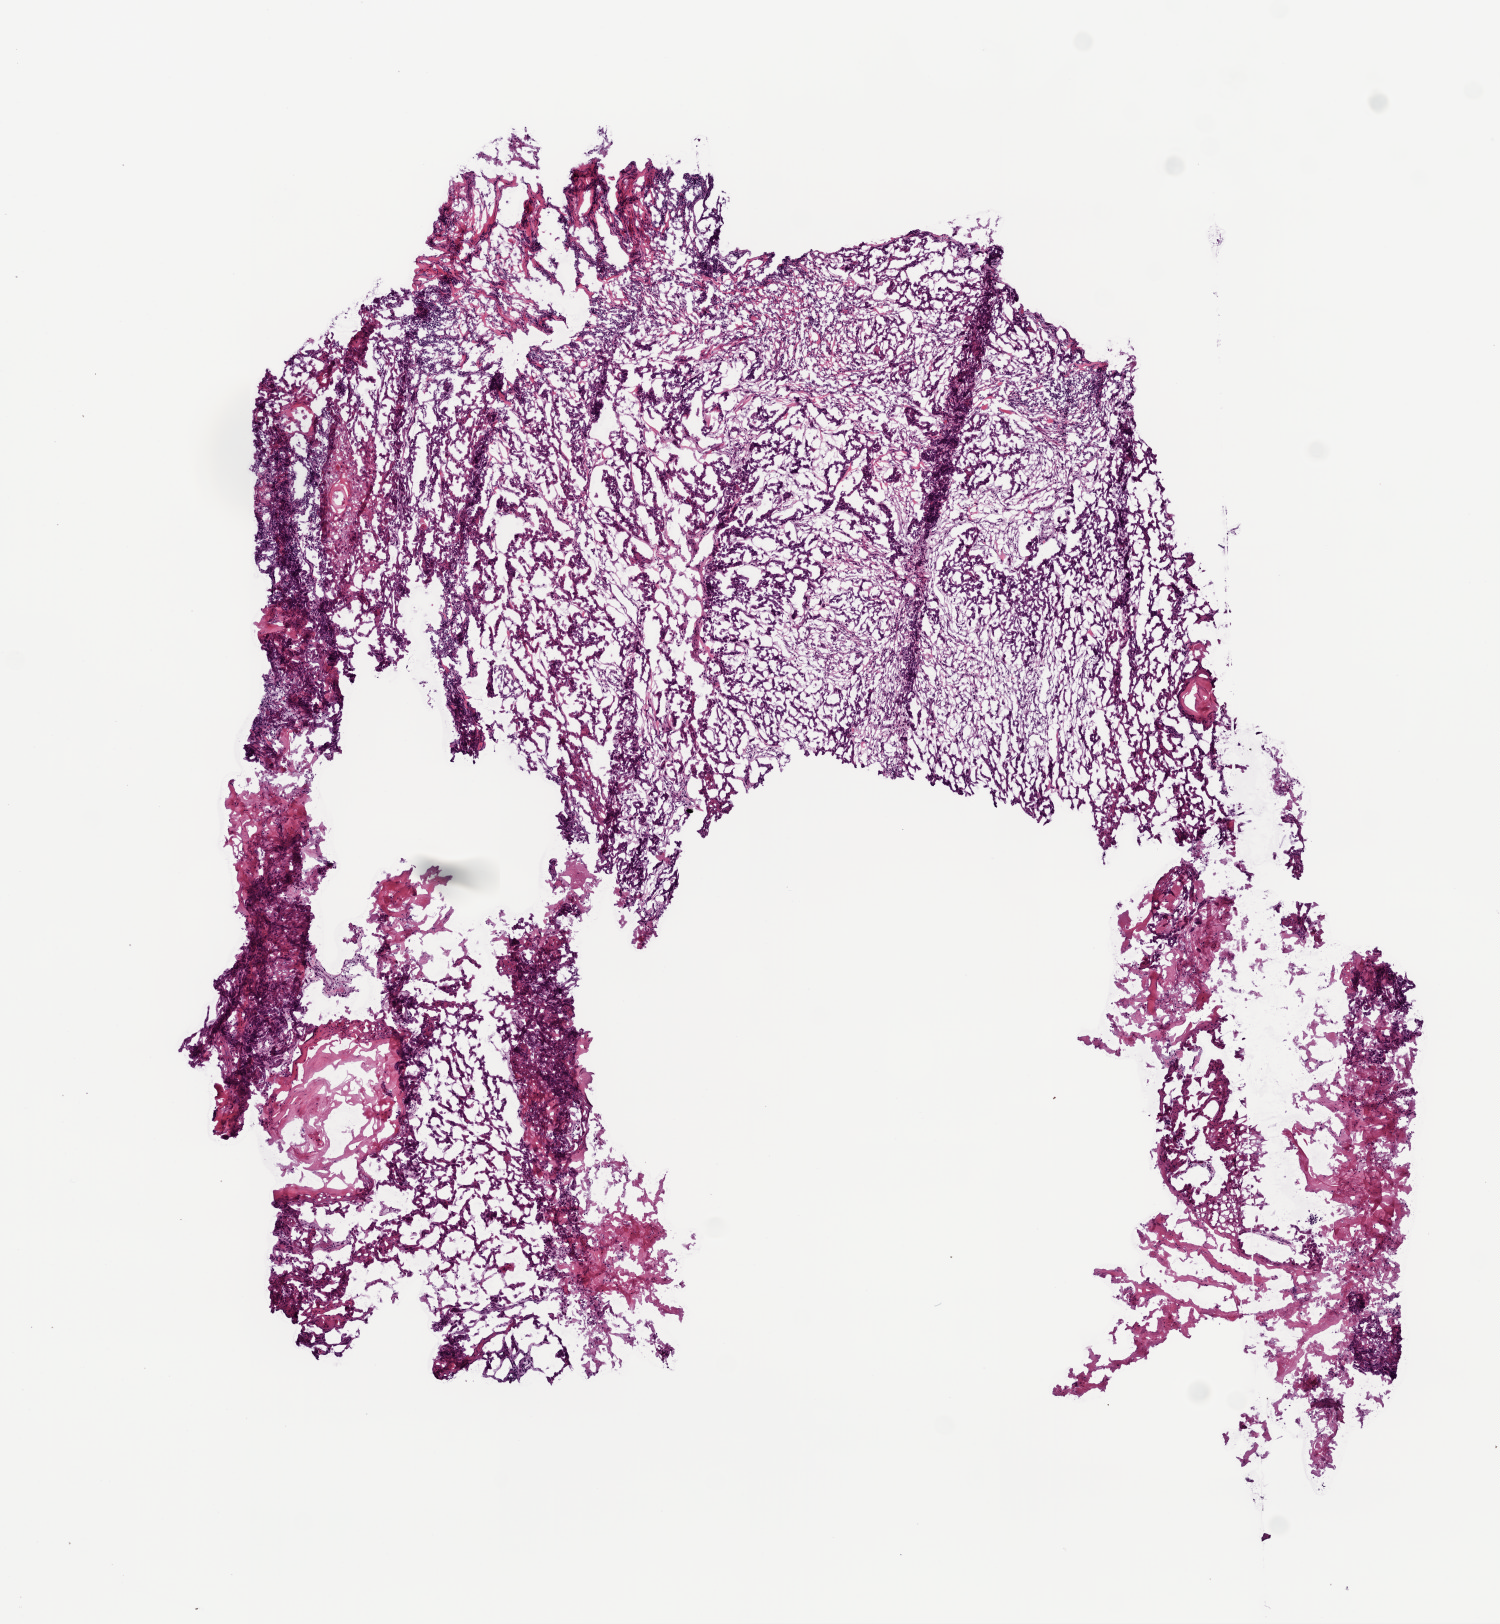
H&E whole-slide image — a low-resolution overview of the entire scanned area, about 6.0 x 6.5 mm (from a 20x scan), frozen section from the bottom of the tissue portion, head and neck, primary tumour sample. Male patient; age at initial diagnosis 58 years. Histologic grade: G3 (poorly differentiated). Pathologist review of this section (percent, as recorded): tumour cells 40%, tumour nuclei 50%, normal cells 0%, stromal cells 60%, necrosis 0%.
AJCC pathologic stage: IVA (7th edition). Pathologic diagnosis: Squamous cell carcinoma, NOS (larynx, NOS).